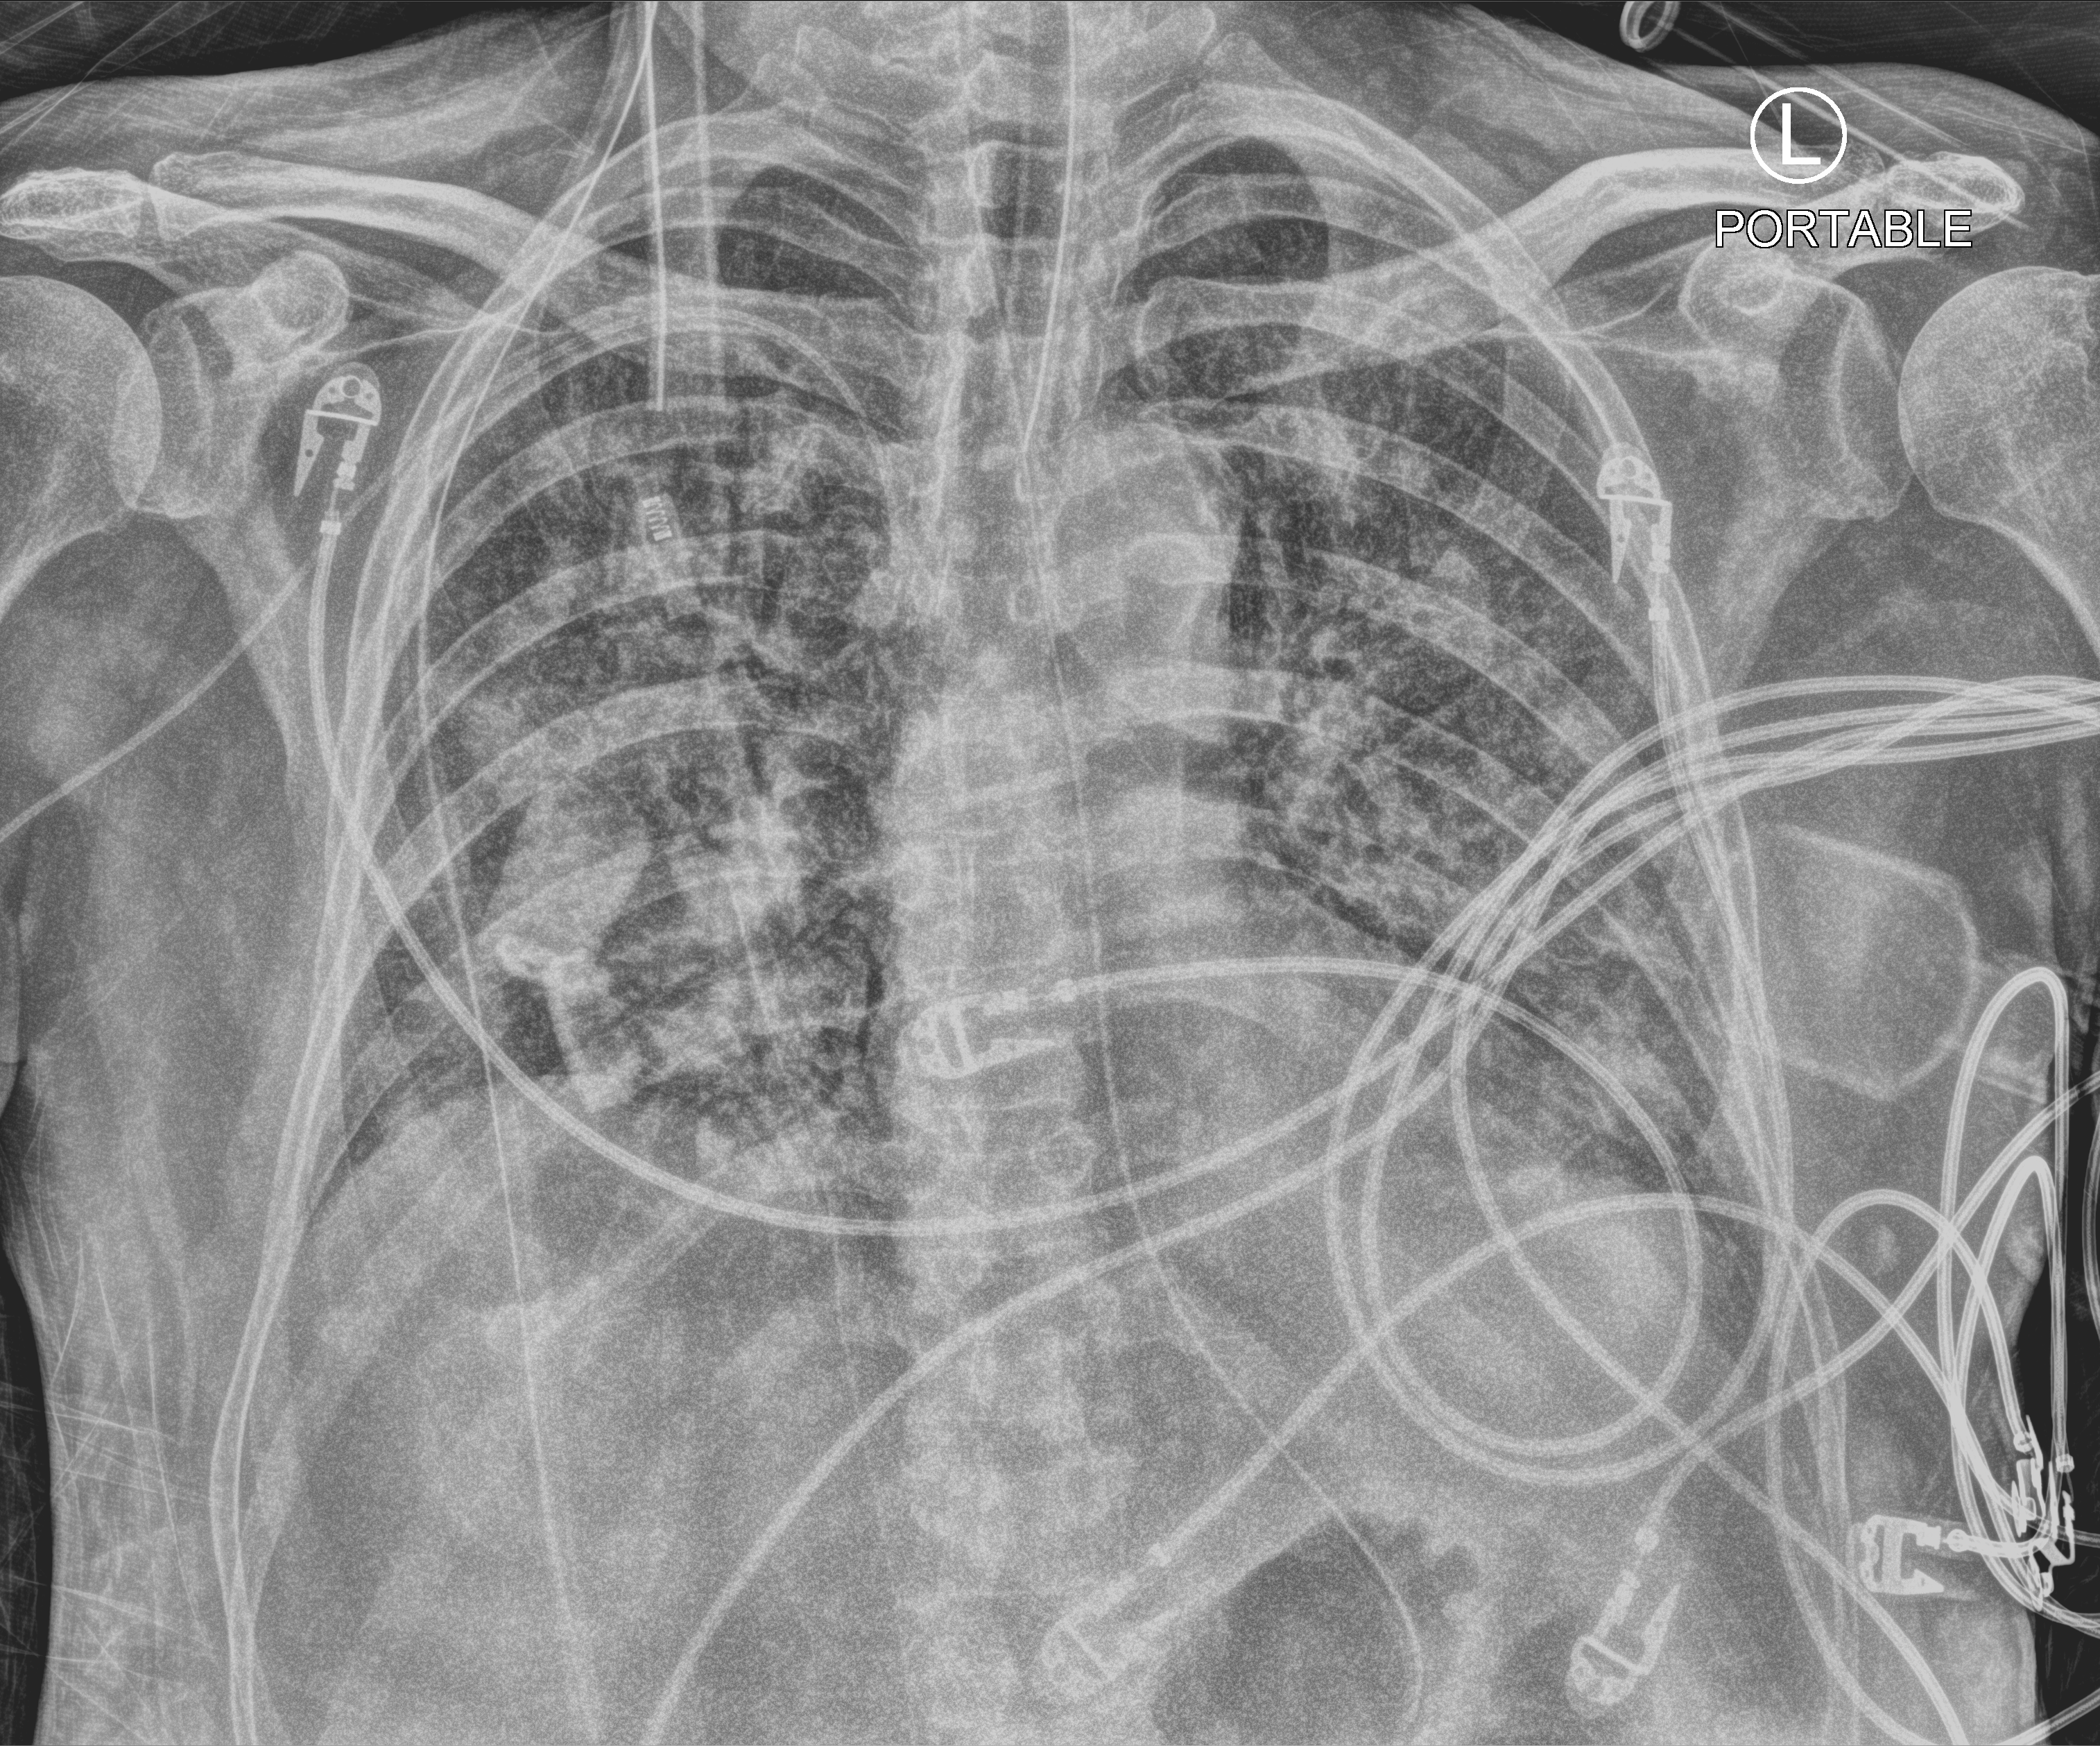
Chest X-ray (portable); anteroposterior (AP) projection. Patient hospitalised with COVID-19; male, aged 60–74 years.
Admission-level facts for this patient (not findings on this image; timing relative to this image not recorded):
- mechanically ventilated during this hospital stay: yes